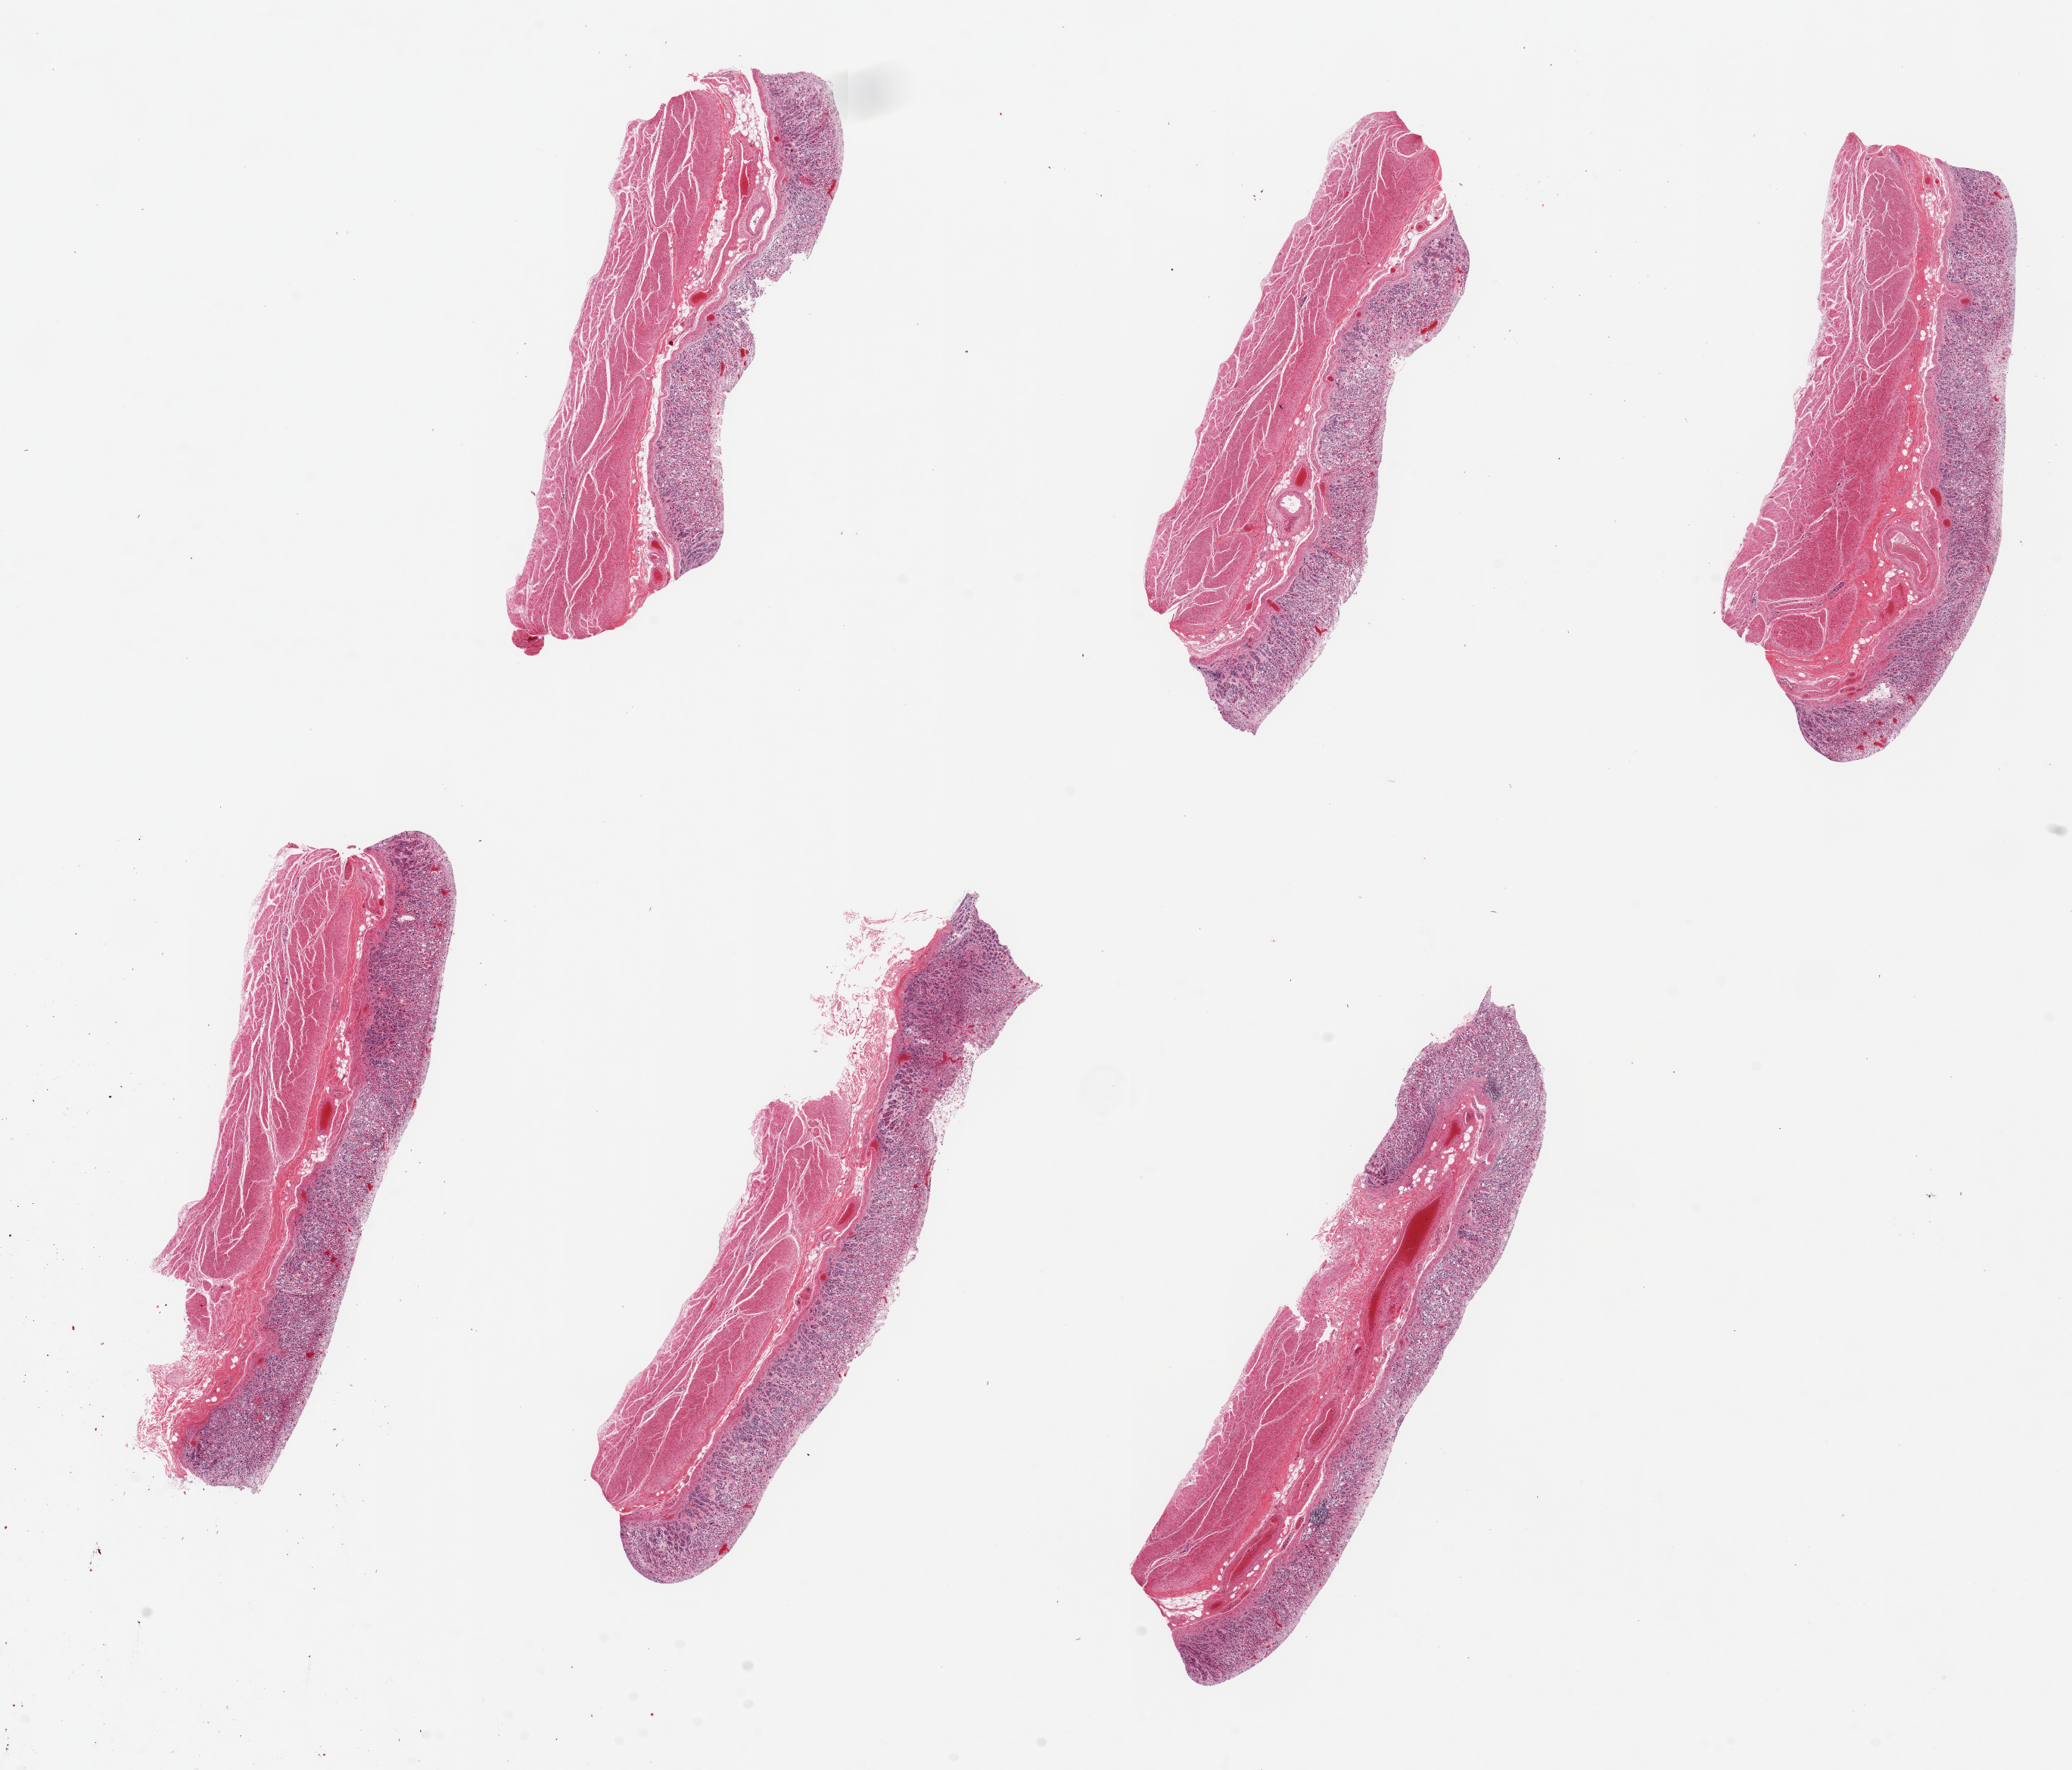
Haematoxylin and eosin whole-slide image, shown as a low-resolution overview of the whole scanned area (about 21.7 x 18.5 mm); PAXgene-fixed paraffin-embedded (PFPE) section; target tissue: stomach; donor tissue sample. Male donor.
Reviewer comment on this tissue sample: 6 pieces, up to 8x2mm.